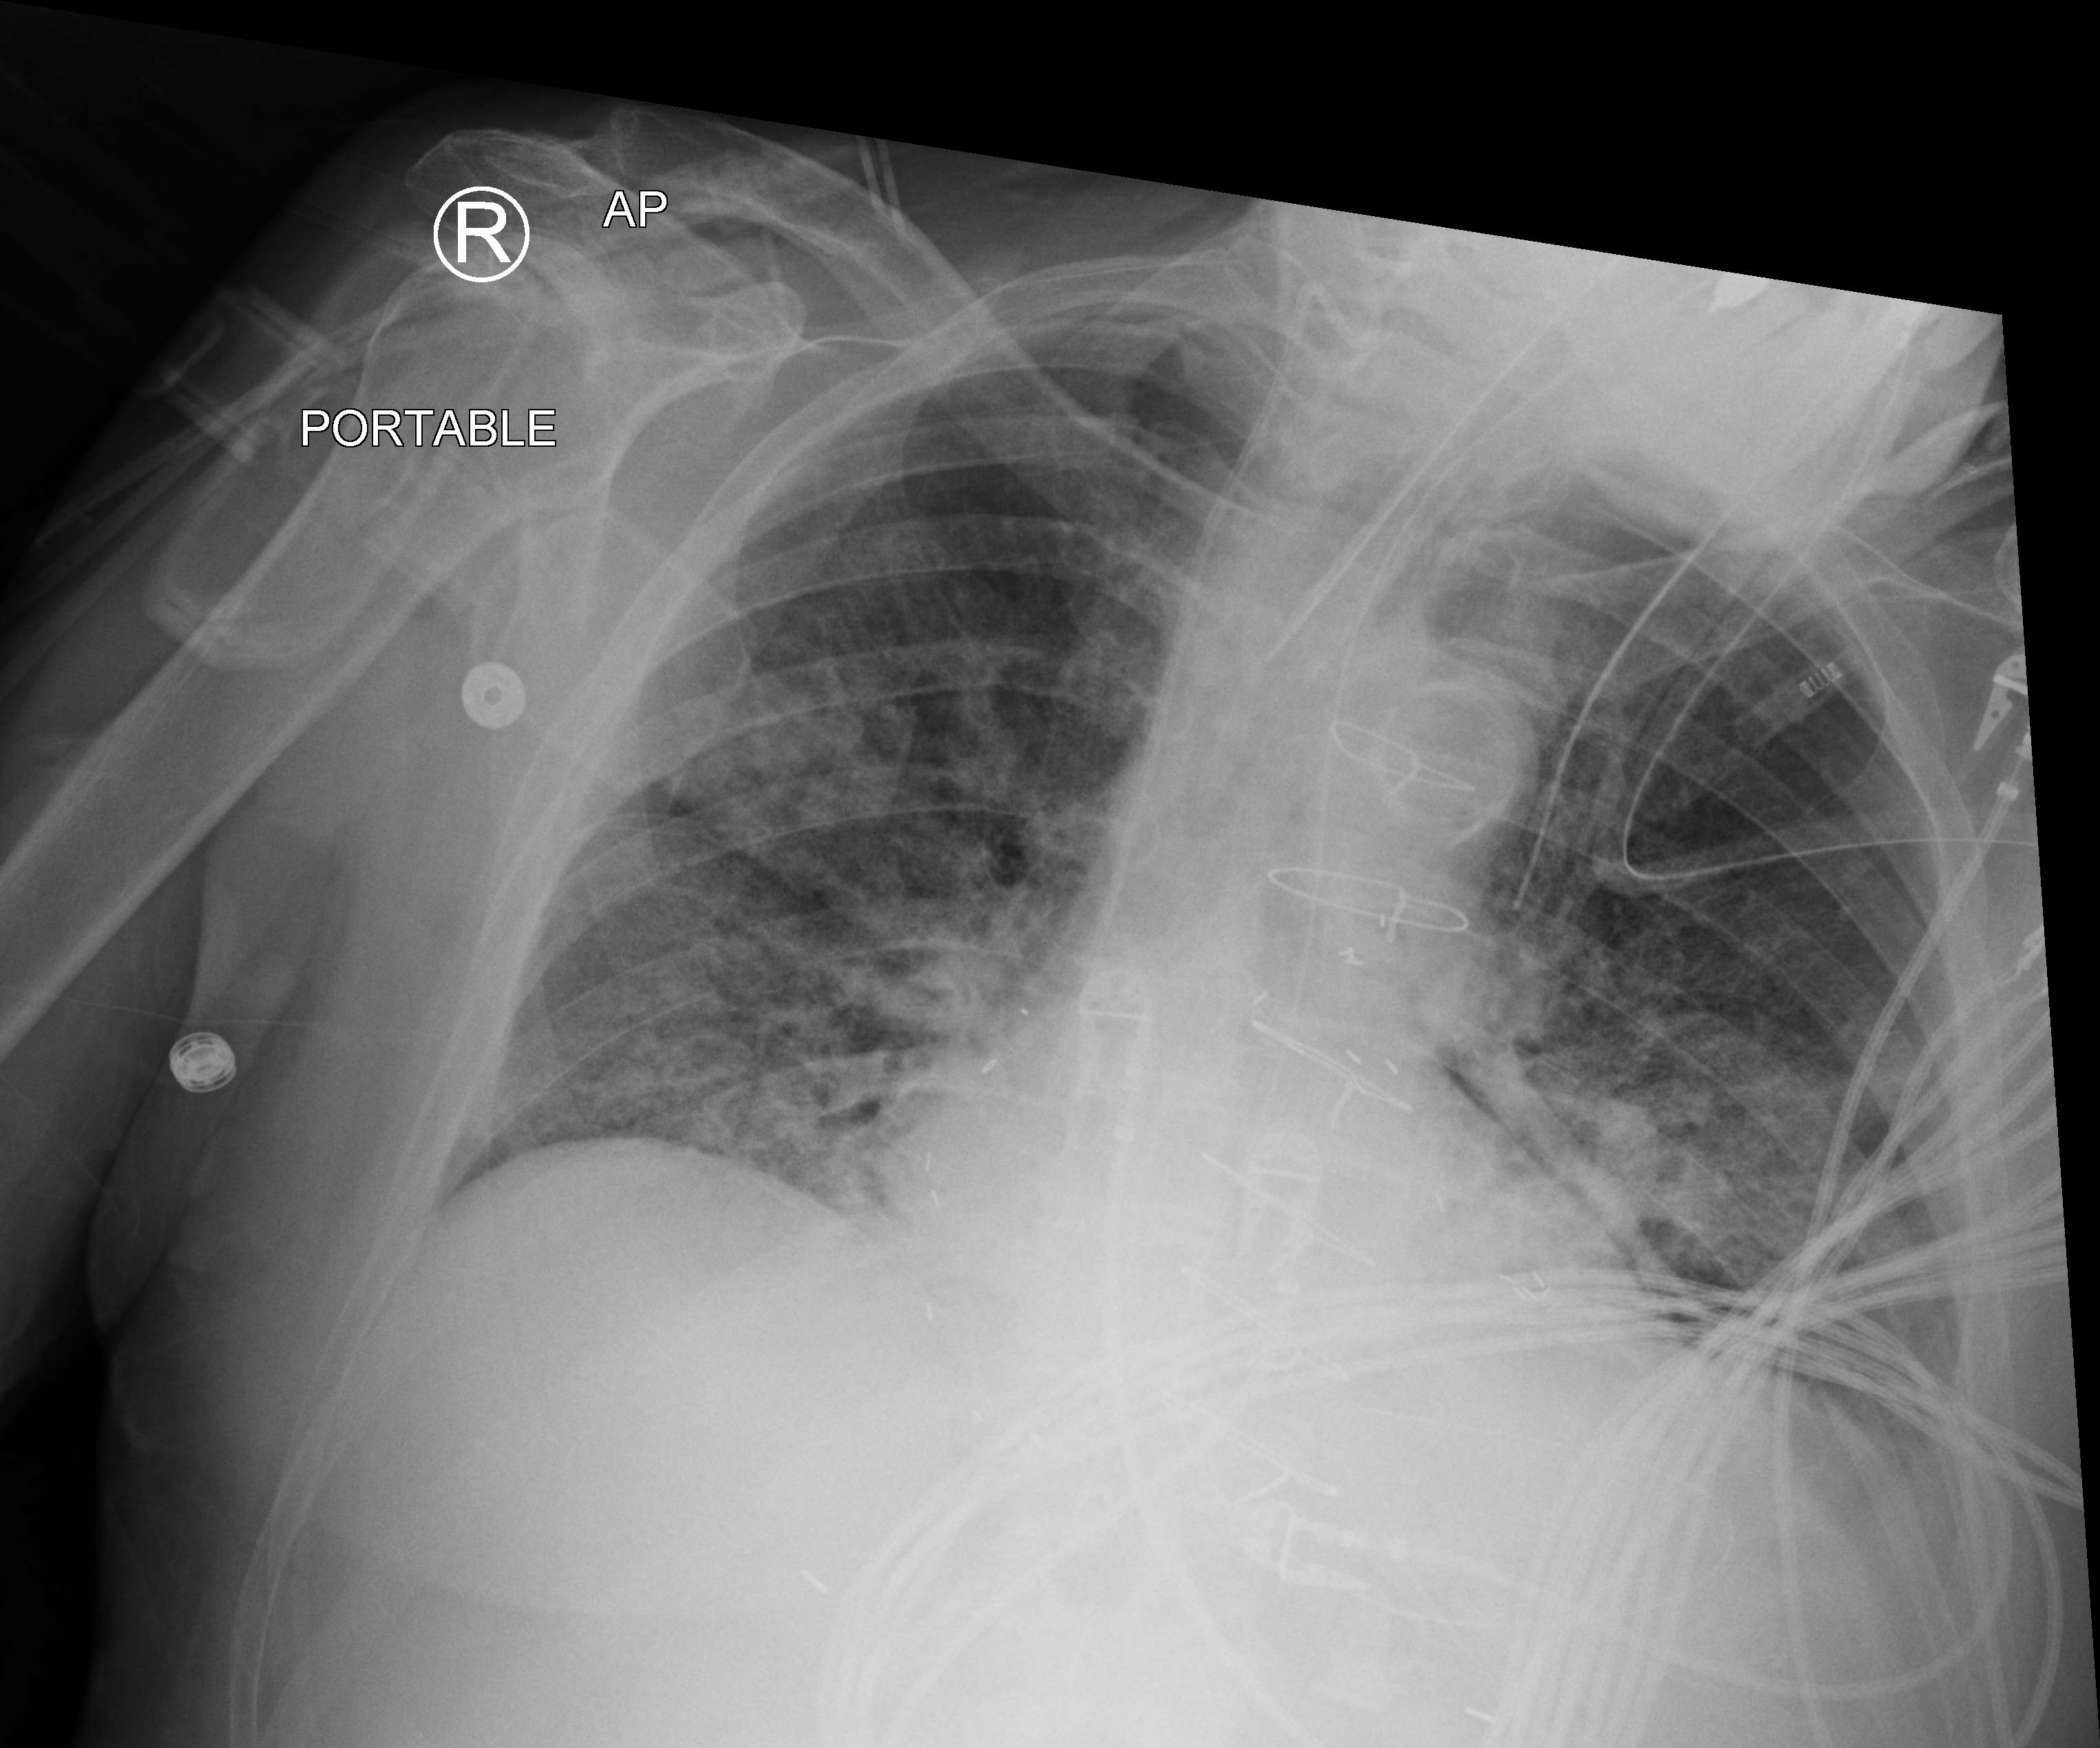
Bedside chest radiograph (computed radiography), anteroposterior (AP) projection. Male patient hospitalised with COVID-19, age 75–90 years.
From the hospital-stay record, not from the radiograph (when in the stay this image was taken is not recorded): admitted to intensive care during this hospital stay: yes; diabetes (admission record): no.